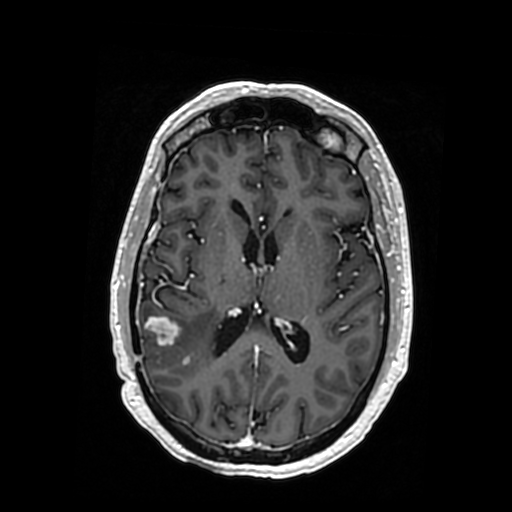
Brain MRI from a brain-tumour surgery series, one axial slice. Slice 170 of 364 in the series (ordered by position). T1-weighted post-contrast. 512 × 512 image matrix, field of view 260 × 260 mm. Case-level facts recorded for this patient, not image findings: histopathology: Oligodendroglioma; WHO grade: 3; IDH mutation: yes; tumour location: Right Posterior Temporal Inferior Parietal.
Outlined on this slice (manually delineated by an expert):
- tumour: bounding box [x1, y1, x2, y2] px = [146, 317, 217, 372]